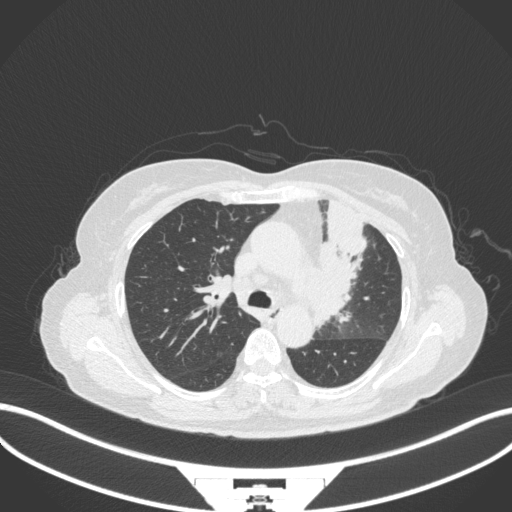
Chest CT, one axial slice; slice 225 of 382 in the series (ordered by position); lung window (W 1500 / L -600 HU); 1 mm slice thickness; 512 × 512 image matrix, field of view 400 × 400 mm. Patient: female, 64 years. Case-level facts recorded for this patient, not image findings: clinical TNM (as recorded): T2a N2 M0.
Outlined on this slice (bounding box drawn by a radiologist):
- lung tumour (recorded histology: adenocarcinoma): bounding box [x1, y1, x2, y2] px = [307, 193, 370, 327]